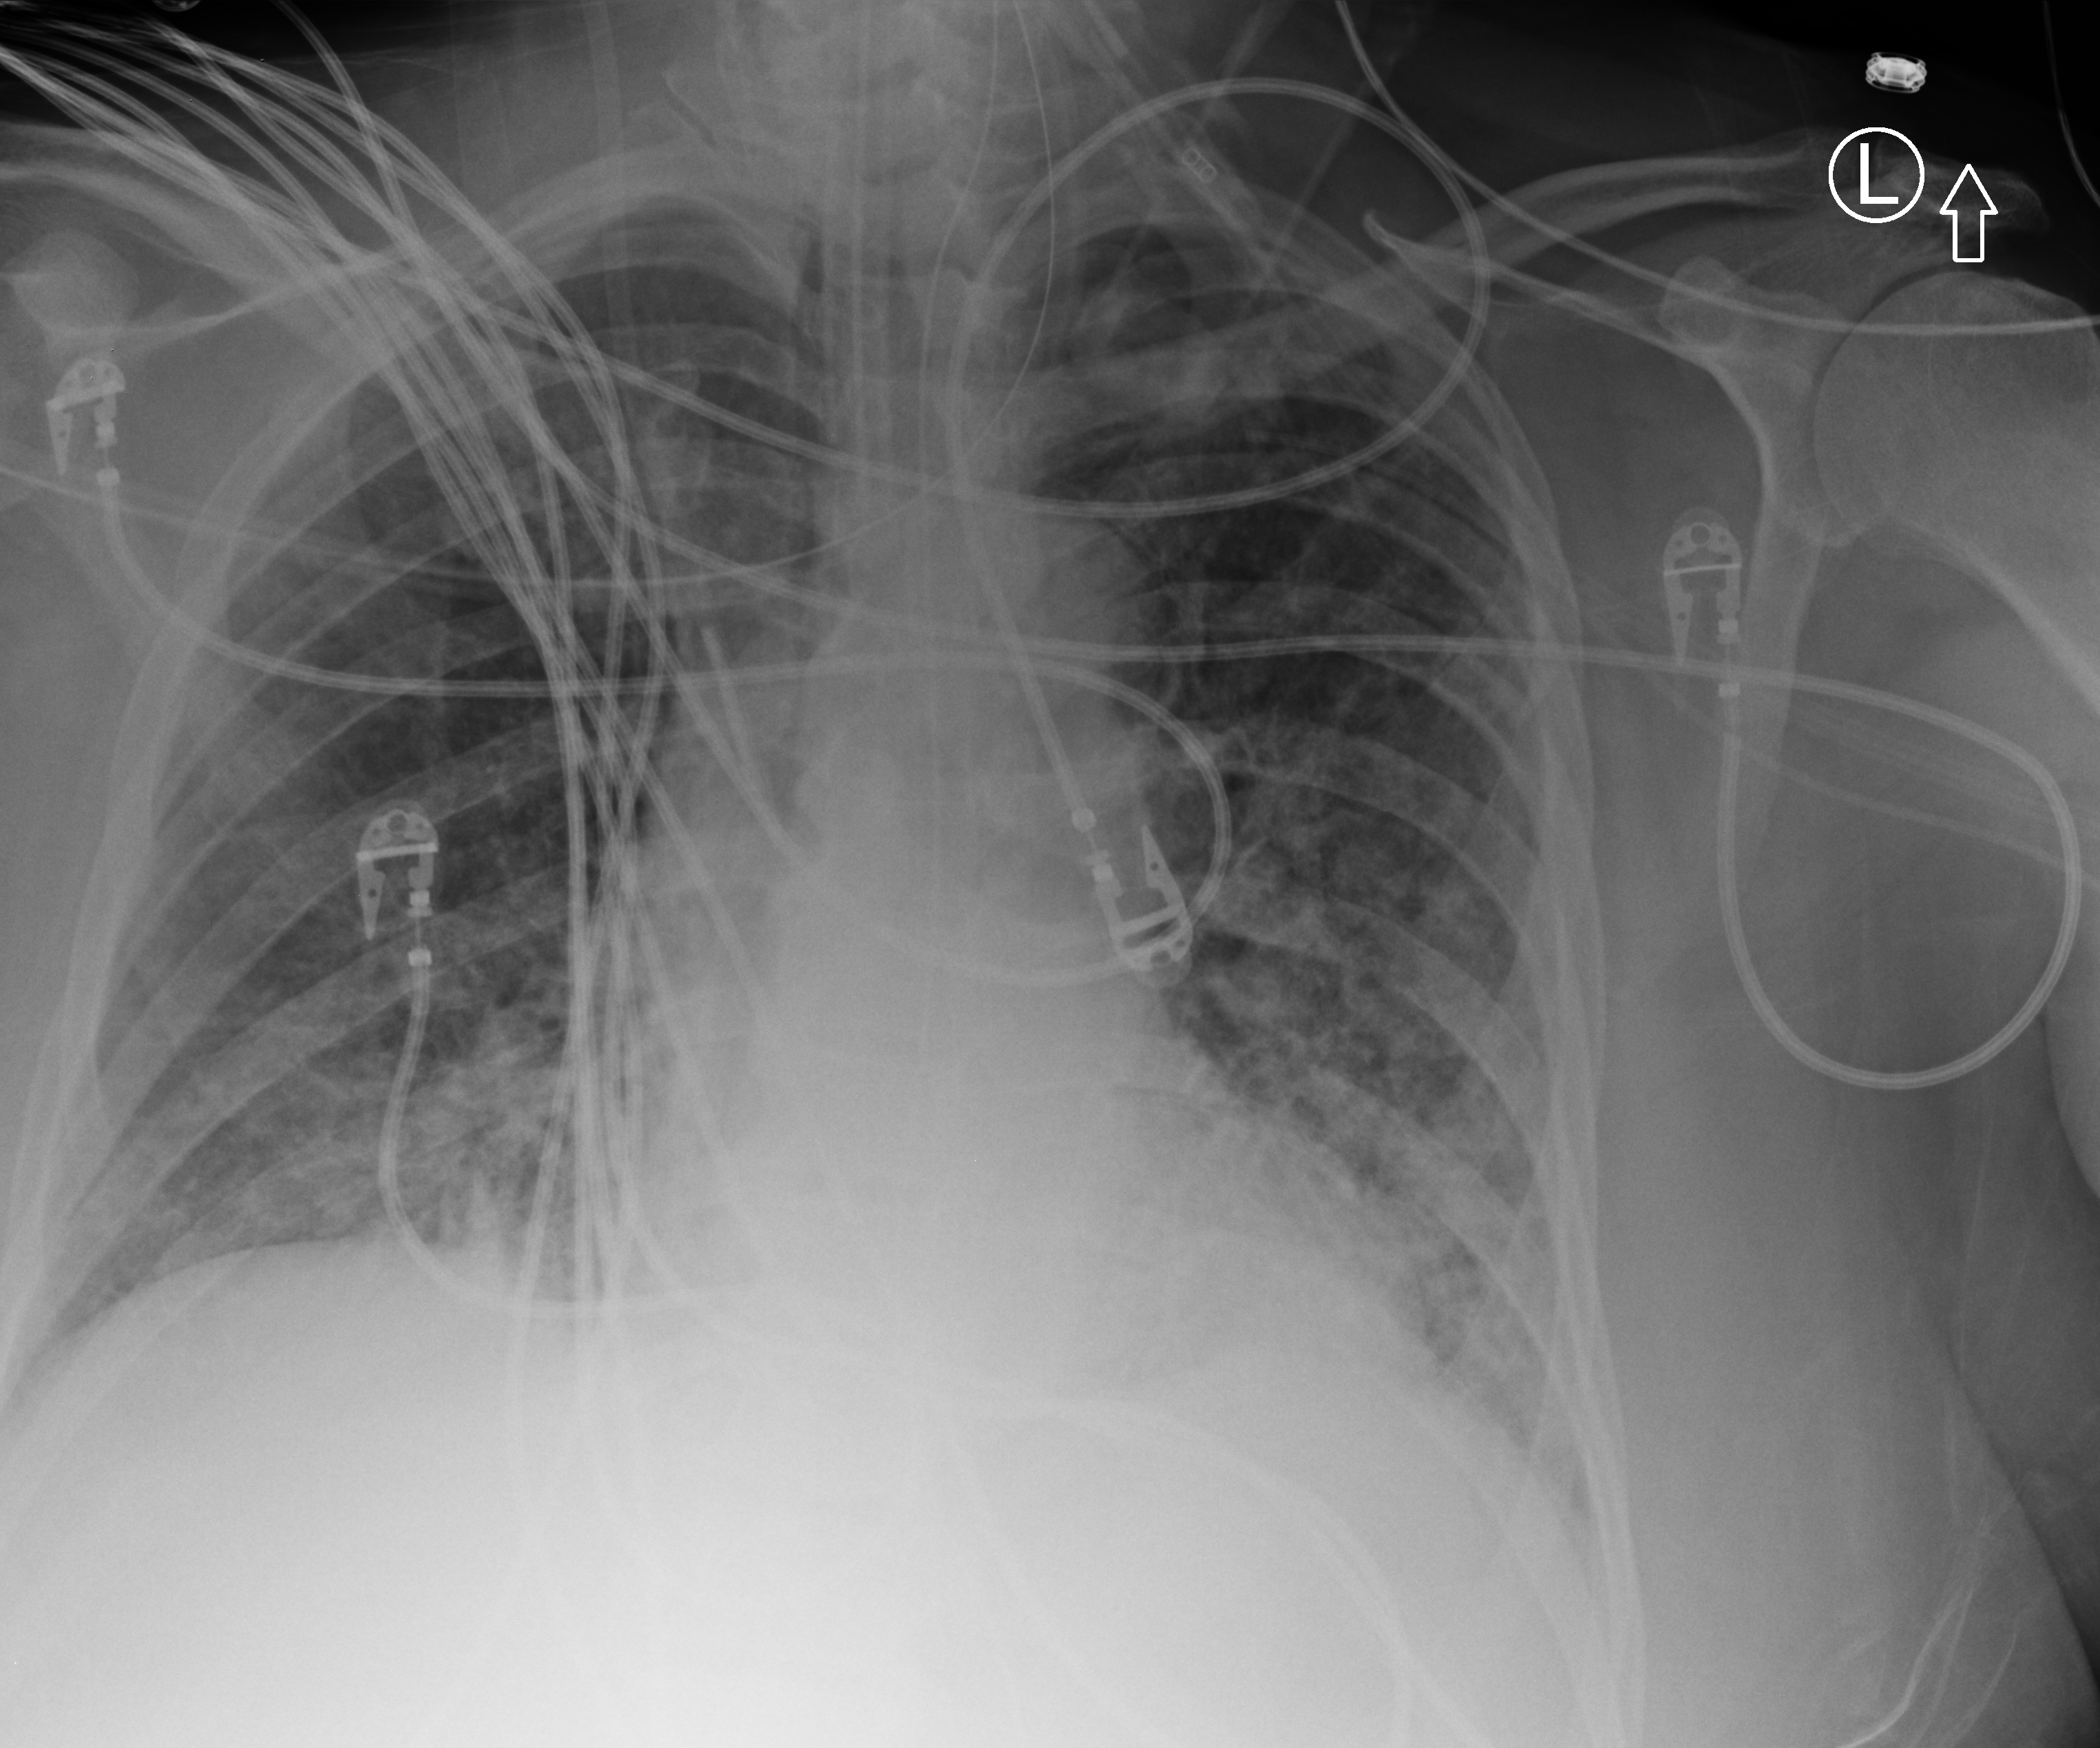
Chest X-ray (portable), anteroposterior (AP) projection. Male patient hospitalised with COVID-19, age 60–74 years.
From the hospital-stay record, not from the radiograph (when in the stay this image was taken is not recorded): other chronic lung disease (admission record): no.